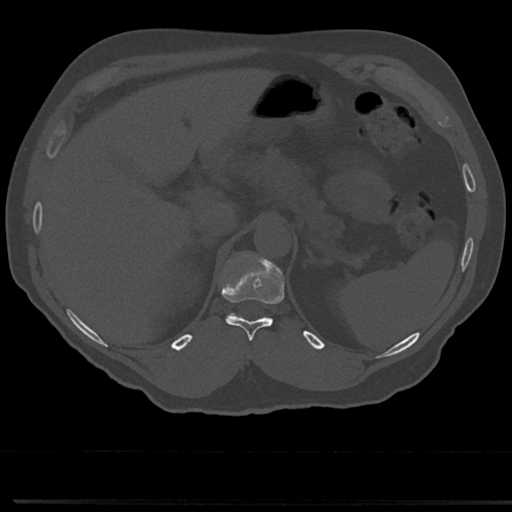
CT including the spine, one axial slice; position 190 of 817 along the scan axis; reconstruction kernel Br40s/3; 120 kVp; bone window (W 1800 / L 400 HU); 0.5 mm slice thickness; 512 × 512 image matrix, field of view 355 × 355 mm. Male patient, age 61 years. From the clinical record (not read from this slice): primary cancer: prostate.
Outlined on this slice (semi-automatically segmented with operator editing):
- T11 vertebra: bounding box [x1, y1, x2, y2] px = [225, 269, 283, 343]
- T12 vertebra: [228, 256, 255, 315]